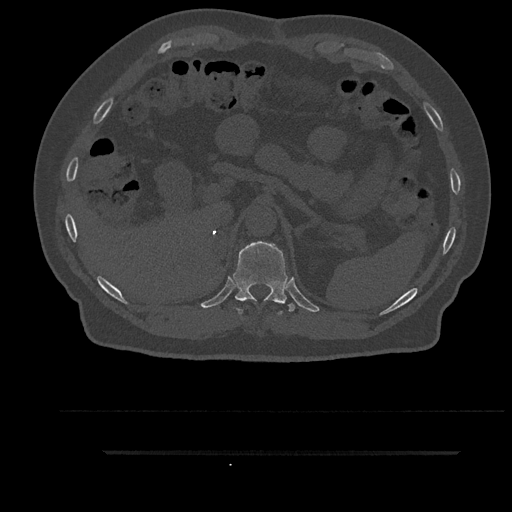
CT including the spine, one axial slice. Slice 321 of 797 in the series (ordered by position). Reconstruction kernel Br40s/3. 120 kVp. Bone window (W 1800 / L 400 HU). 0.5 mm slice thickness. 512 × 512 image matrix. Male patient, age 63 years. From the clinical record (not read from this slice): primary cancer: renal.
Annotated regions visible in this slice (semi-automatically segmented with operator editing):
- T11 vertebra: box from (x=233, y=241) to (x=295, y=314) px